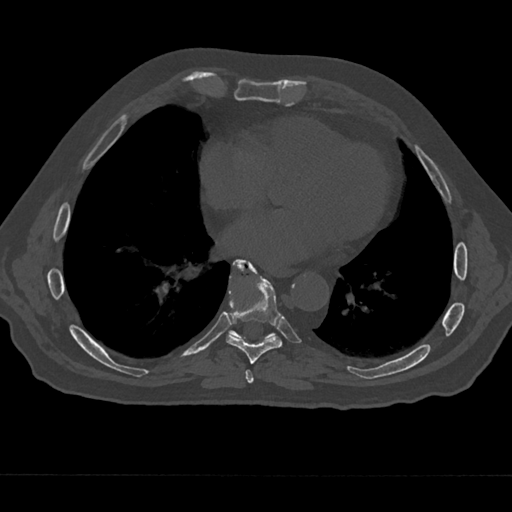
CT including the spine, one axial slice; position 303 of 797 along the scan axis; bone window (W 1800 / L 400 HU); 0.5 mm slice thickness; 512 × 512 image matrix, field of view 377 × 377 mm. Male patient, age 75 years. From the clinical record (not read from this slice): primary cancer: renal.
Structures marked on this image (semi-automatically segmented with operator editing):
- T7 vertebra: bounding box (x1, y1, x2, y2) in pixels: (241, 367, 255, 384)
- T8 vertebra: (226, 263, 283, 364)
- T9 vertebra: (229, 259, 276, 339)